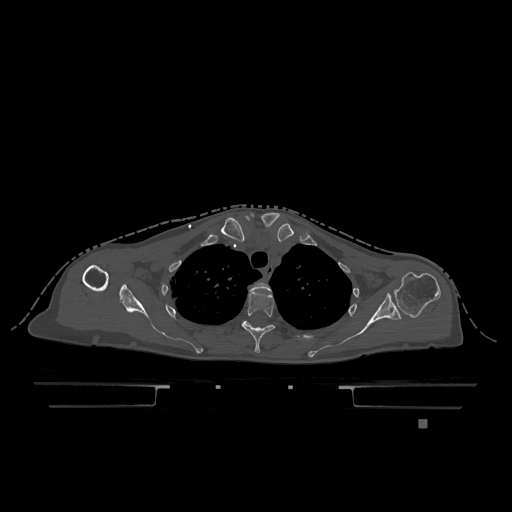
CT including the spine, one axial slice. Position 921 of 1317 along the scan axis. Bone window (W 1800 / L 400 HU). 0.5 mm slice thickness. 512 × 512 image matrix, field of view 500 × 500 mm. Female patient, age 74 years. From the clinical record (not read from this slice): primary cancer: lung; vertebrae with lytic lesions (as recorded): T1, T4, T5, T6, L4, L5.
Annotated regions visible in this slice (semi-automatically segmented with operator editing):
- T2 vertebra: bounding box <250,282,271,292> (left, top, right, bottom; pixels)
- T3 vertebra: <241,291,275,353>
- T4 vertebra: <244,321,307,339>